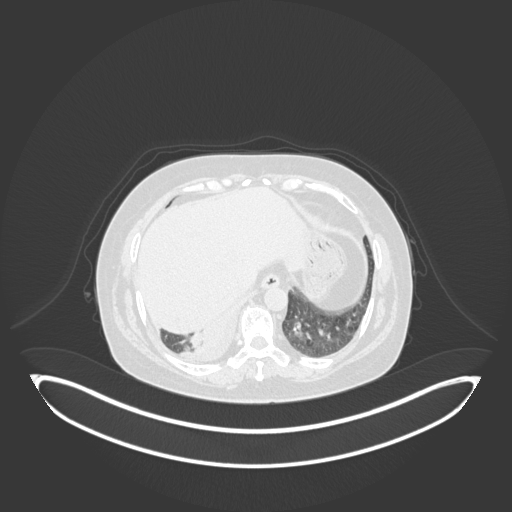
Chest CT, one axial slice; slice 25 of 231 in the series (ordered by position); 120 kVp; lung window (W 1500 / L -600 HU); 1 mm slice thickness; 512 × 512 image matrix, field of view 500 × 500 mm. Female patient, age 56 years. From the clinical record (not read from this slice): clinical TNM (as recorded): T2b N1 M0; histopathological grade: G3.
Outlined on this slice (rectangle marked by the reading radiologist):
- lung tumour (recorded histology: small cell carcinoma): bounding box [x1, y1, x2, y2] px = [183, 321, 215, 353]